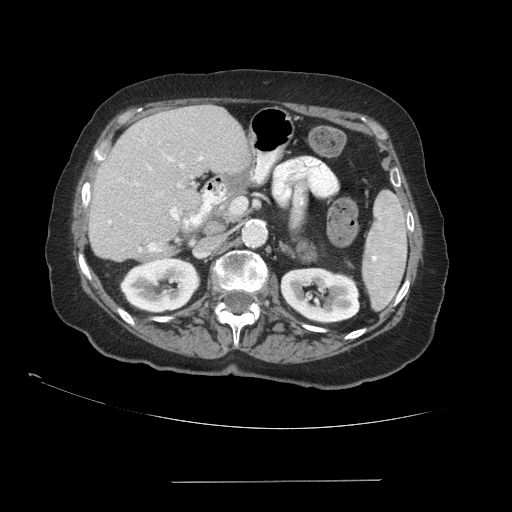
Contrast-enhanced abdominal CT (liver protocol), one axial slice. Slice 49 of 89 in the series (ordered by position). Reconstruction kernel STANDARD. Soft-tissue window (W 400 / L 40 HU). 2.5 mm slice thickness. 512 × 512 image matrix, field of view 400 × 400 mm. From the clinical record (not read from this slice): diagnosis: hepatocellular carcinoma (patient treated with transarterial chemoembolisation; whether this scan precedes or follows treatment is not stated here); TNM stage (as recorded): Stage-IVA; Child-Pugh class: A; tumour differentiation: poorly differentiated; tumour nodularity: uninodular.
Annotated regions visible in this slice (semi-automatic segmentation, software-assisted and operator-edited):
- liver parenchyma outside the tumour (the mass and vessels are separate outlines, so this box may not span the whole liver): bounding box (x1, y1, x2, y2) in pixels: (88, 104, 250, 260)
- liver vessels: (108, 156, 203, 252)